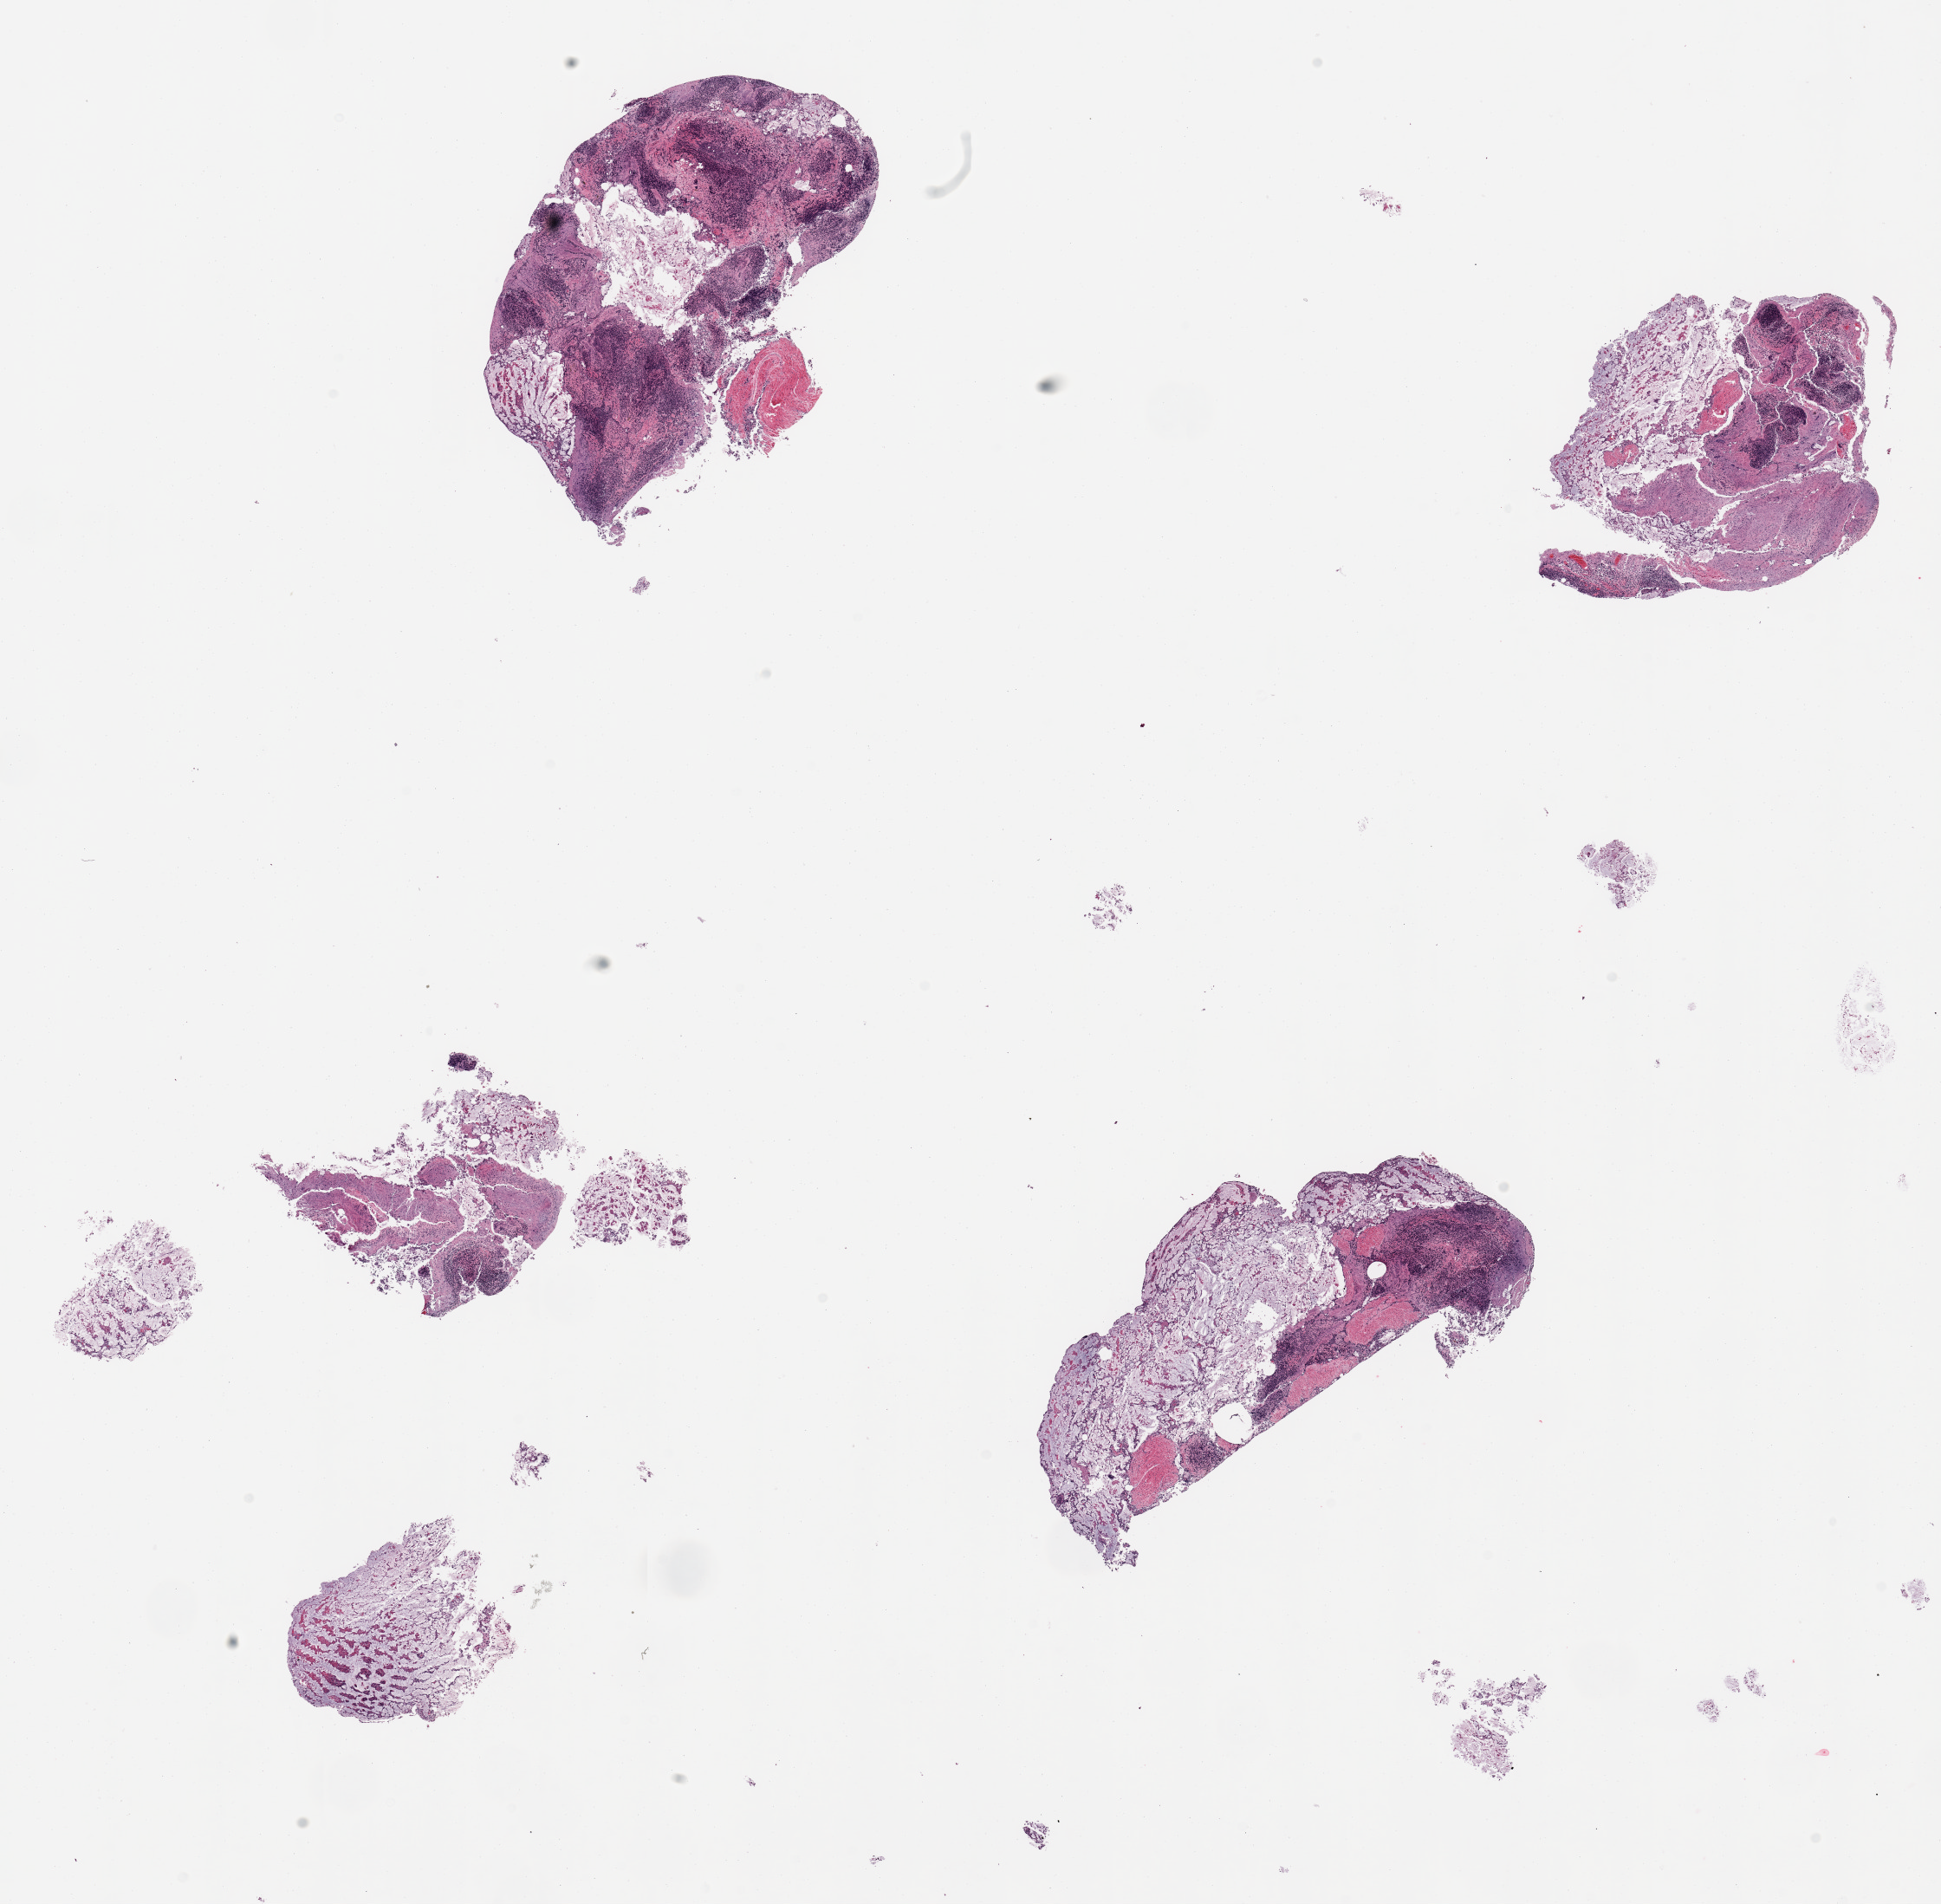
Digitized H&E-stained section — low-resolution overview of the scanned area, about 17.7 x 17.4 mm (slide scanned at 20x), PAXgene-fixed, paraffin-embedded tissue, section of ileum (target tissue), donor tissue sample. Donor sex: female.
Reviewer comment on this tissue sample: 4 pieces, glandular mucosa totally autolyzed, ~20% residuum is lymphoid aggregates.